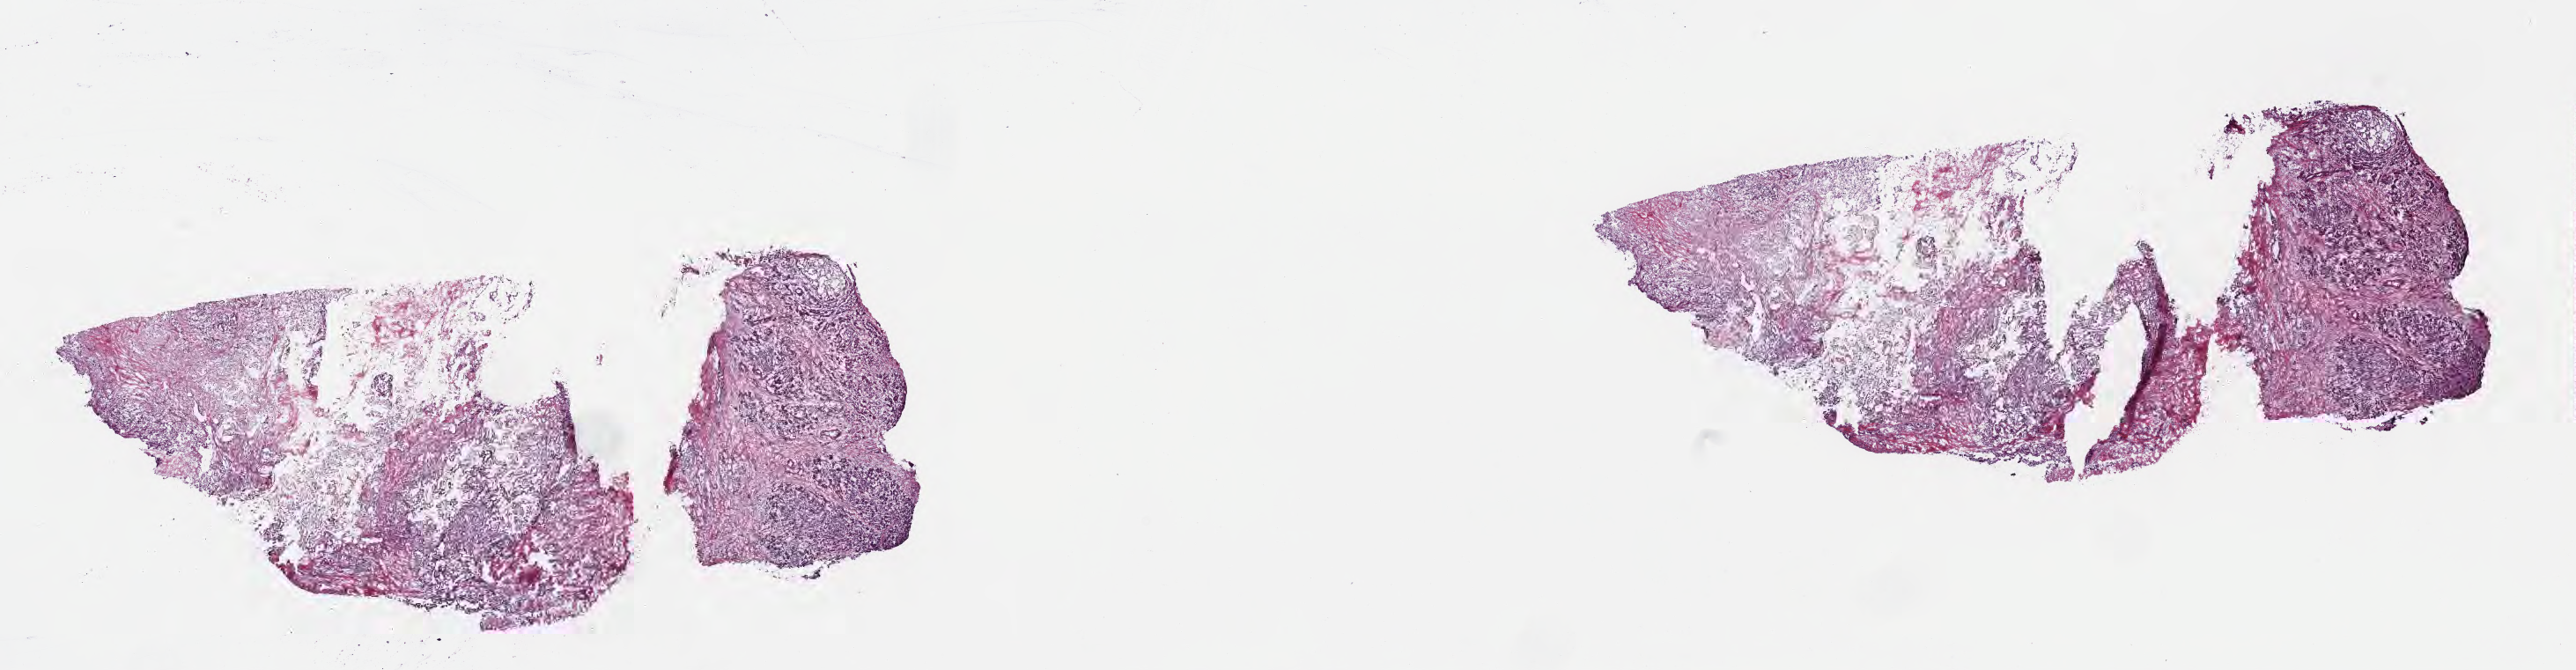
Whole-slide image, haematoxylin and eosin stain — shown as a low-resolution overview of the whole scanned area (about 23.6 x 6.2 mm); cryosection; primary tumor; anatomic site: head of pancreas. Male patient; age at initial diagnosis 57 years. Tumor grade: G2 (moderately differentiated). Pathologist review of this section (percent, as recorded): tumor cells 39%, tumor nuclei 65%, stromal cells 40%, necrosis 5%, normal cells 16%. Infiltration values recorded for this section: lymphocyte infiltration 20%, monocyte infiltration 3%, neutrophil infiltration 0%.
Histologic diagnosis: Infiltrating duct carcinoma, NOS. AJCC pathologic stage: Stage III.